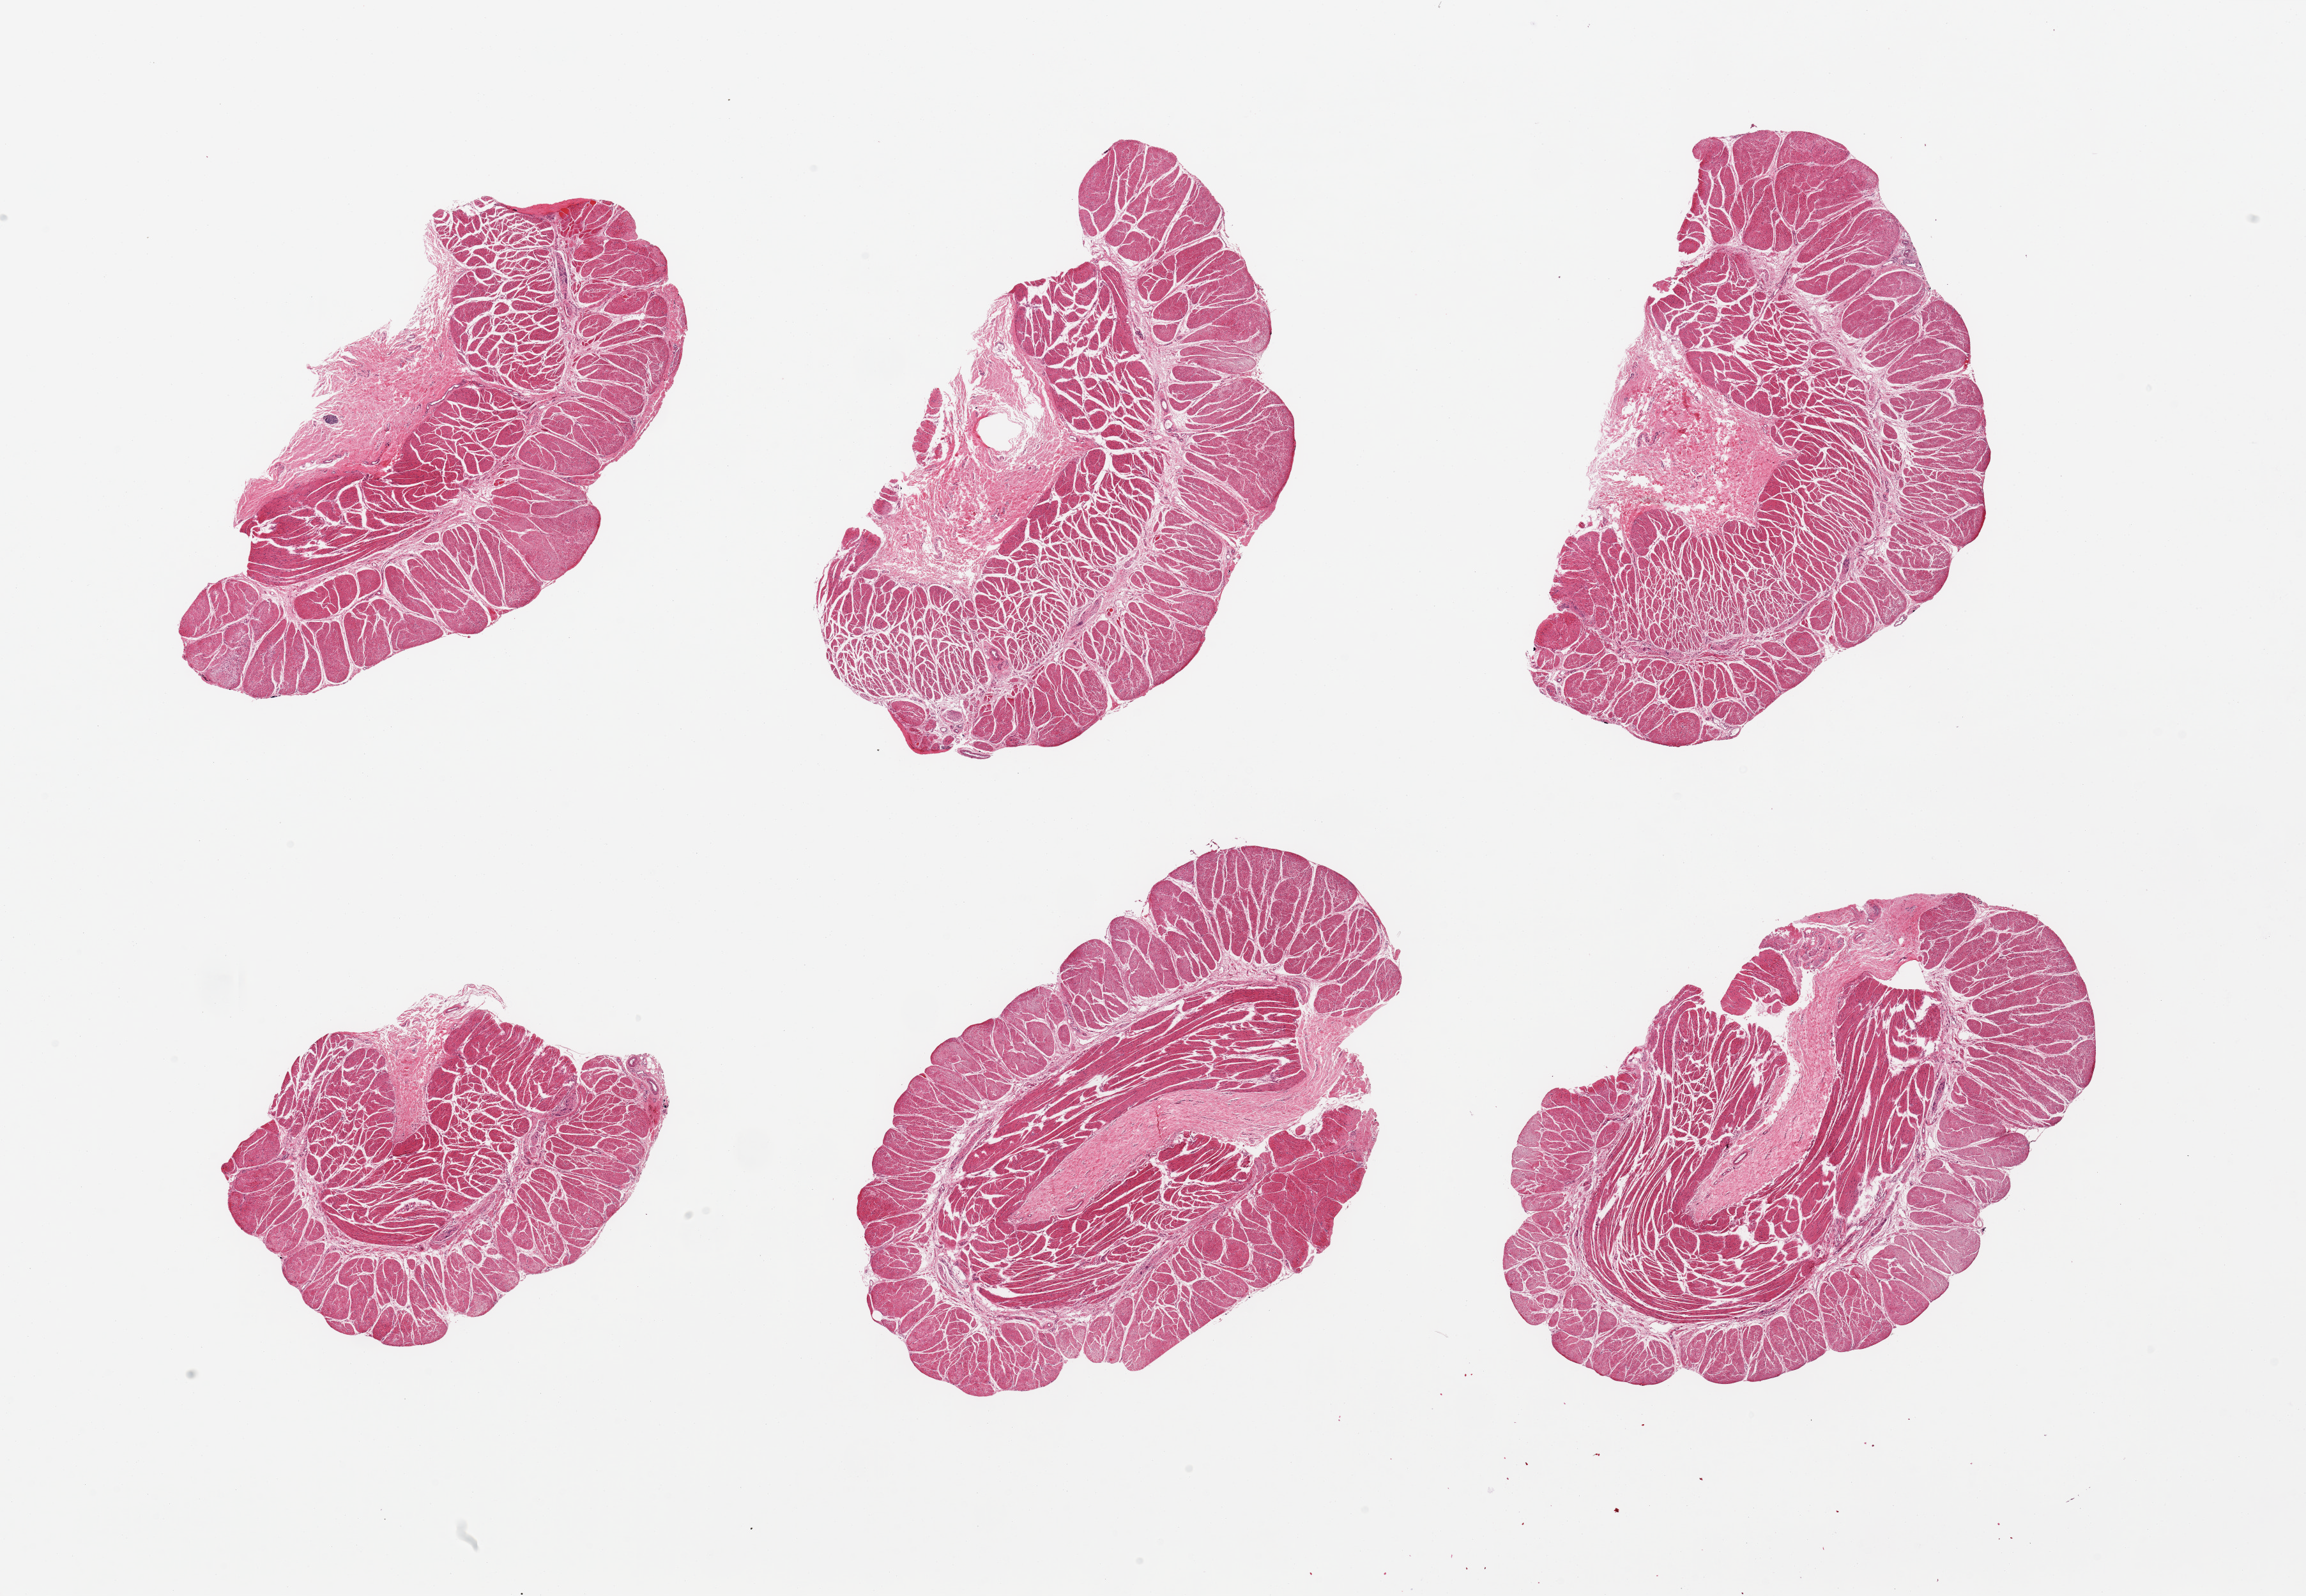
Digitized haematoxylin and eosin-stained section — a low-resolution overview of the entire scanned area, about 28.5 x 19.8 mm. PAXgene-fixed, paraffin-embedded tissue. Section of esophageal muscle (target tissue). Donor tissue sample. Donor: female.
Review note (as recorded): 6 pieces target muscularis.